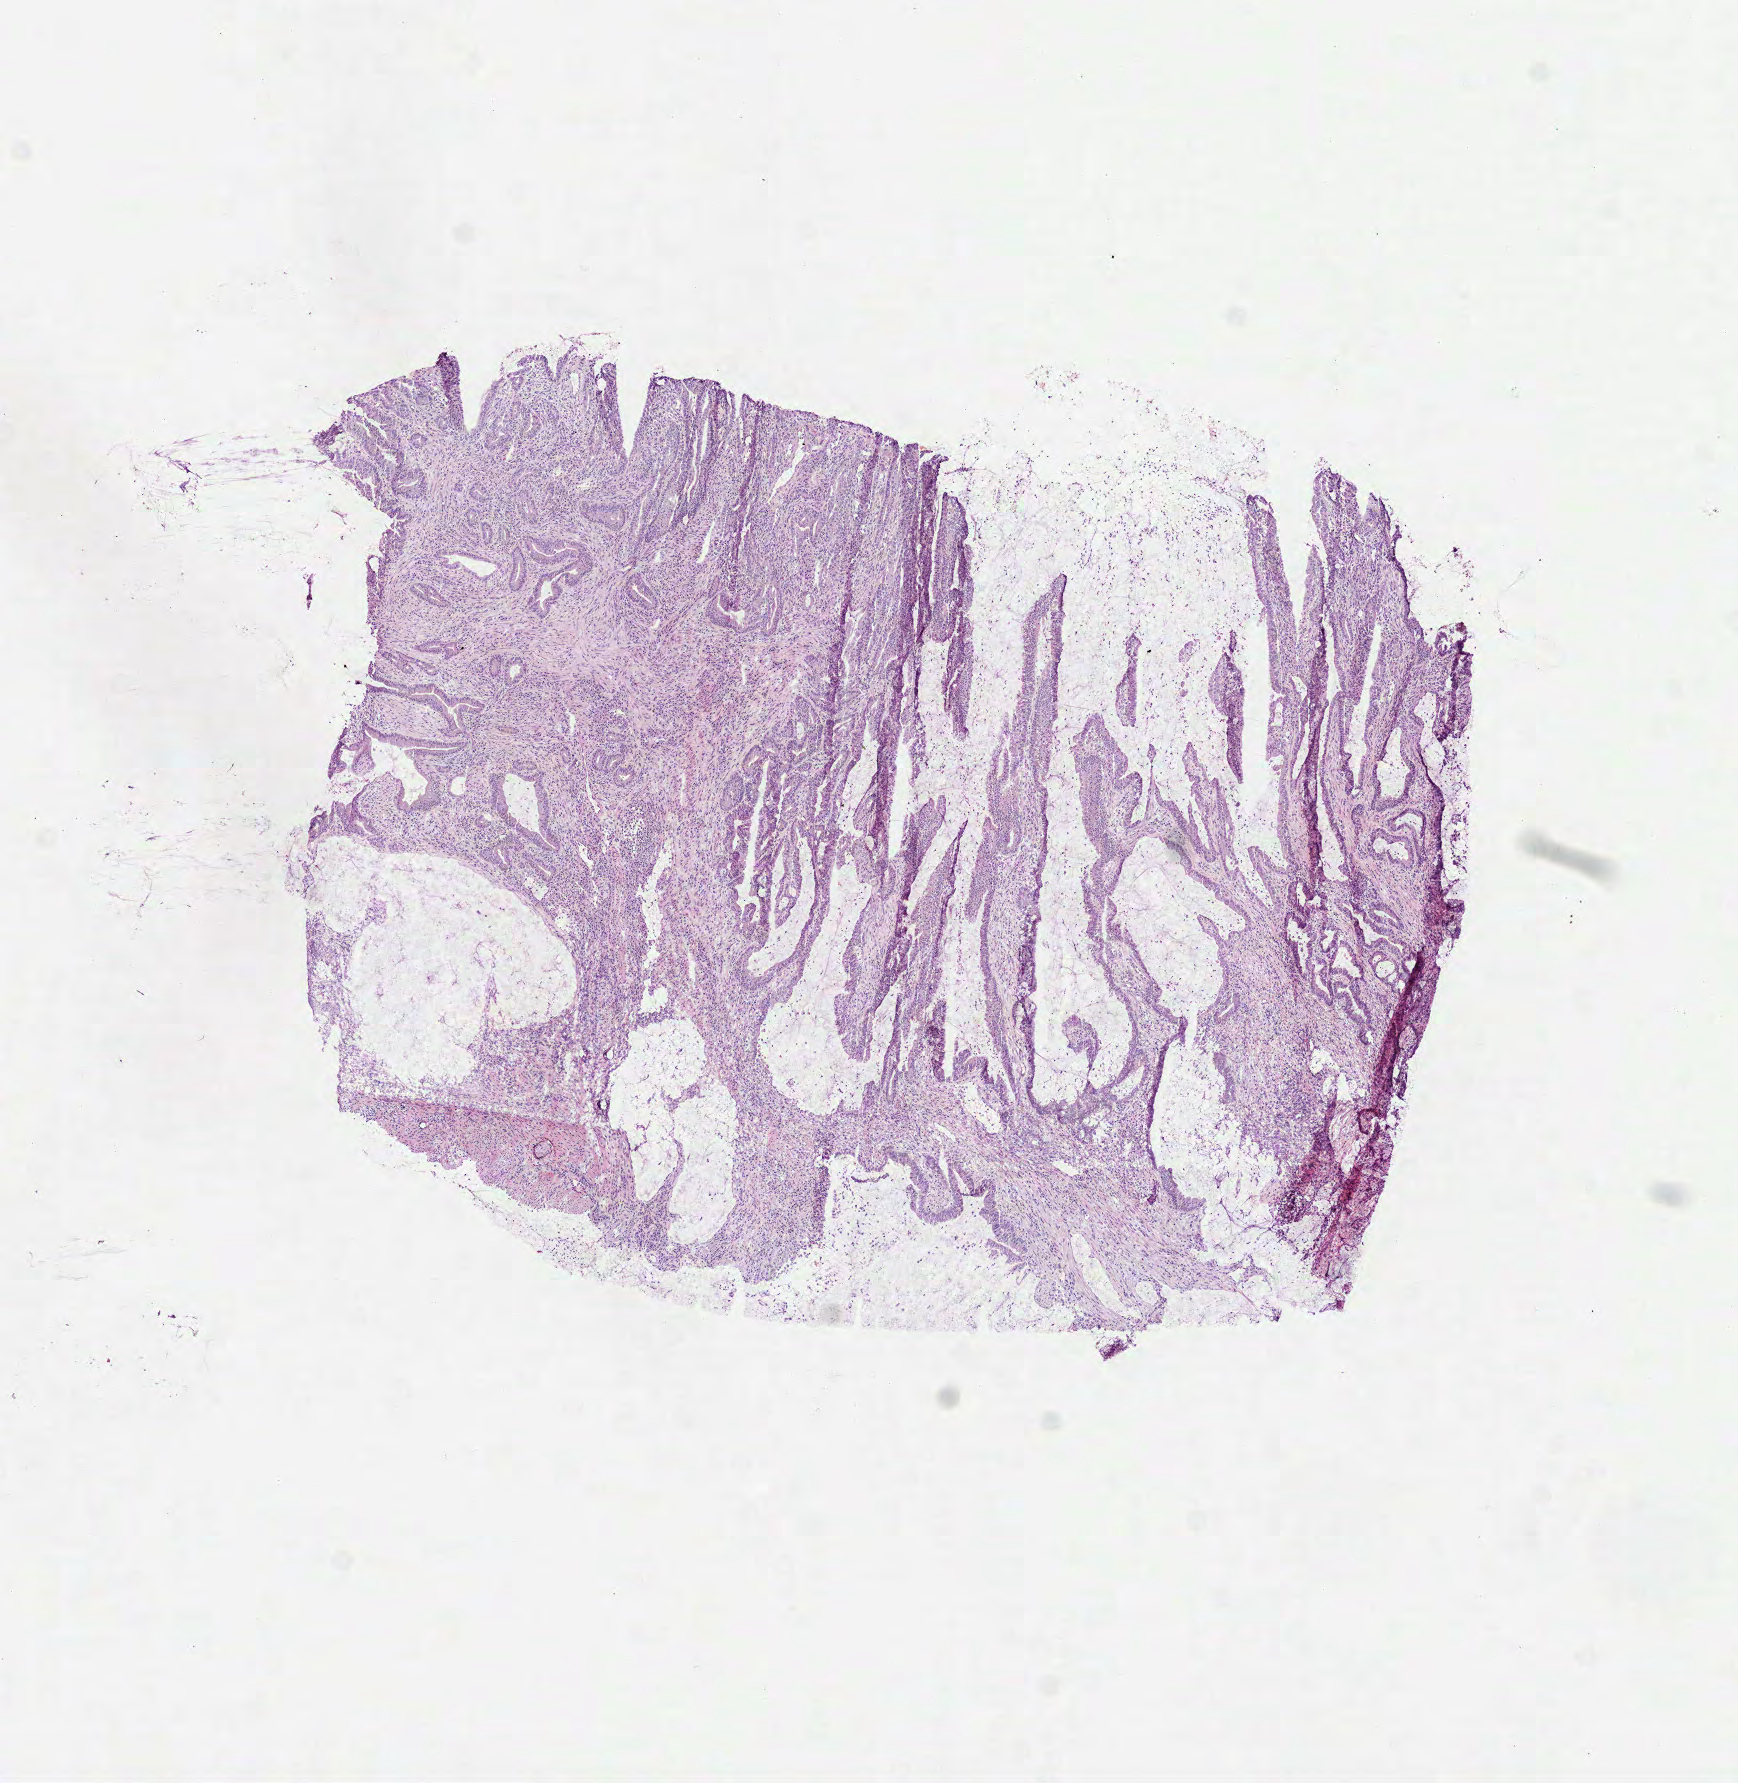
Digitized Hematoxylin and eosin (H&E) stained tissue section (whole slide) — low-resolution overview of the scanned area, about 7.0 x 7.2 mm. Frozen section from the top of the tissue portion. Primary tumour sample from the colon. Male, age 67 years at initial diagnosis. Slide review estimates, as recorded: tumour cells 65%, tumour nuclei 65%, normal cells 0%, stromal cells 34%, necrosis 1%. Infiltration values recorded for this section: lymphocyte infiltration 15%, monocyte infiltration 0%, neutrophil infiltration 3%.
AJCC pathologic stage: IIA (7th edition). Lymph nodes positive (case pathology): 0 of 20 examined. TNM: T3 N0 M0. Diagnosis: Mucinous adenocarcinoma (cecum).